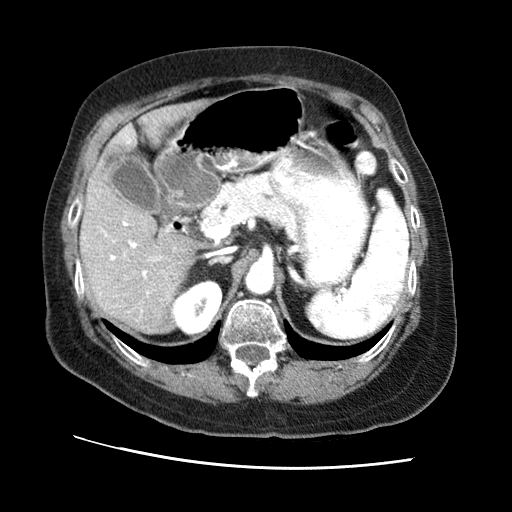
Contrast-enhanced abdominal CT (liver protocol), one axial slice; position 34 of 65 along the scan axis; 120 kVp; soft-tissue window (W 400 / L 40 HU); 2.5 mm slice thickness; 512 × 512 image matrix. From the clinical record (not read from this slice): diagnosis: hepatocellular carcinoma (patient treated with transarterial chemoembolisation; whether this scan precedes or follows treatment is not stated here); TNM stage (as recorded): Stage-II; Child-Pugh class: A.
Outlined on this slice (semi-automatically segmented with operator editing):
- liver parenchyma outside the tumour (the mass and vessels are separate outlines, so this box may not span the whole liver): bounding box [x1, y1, x2, y2] px = [80, 100, 204, 332]
- liver vessels: [100, 134, 162, 312]